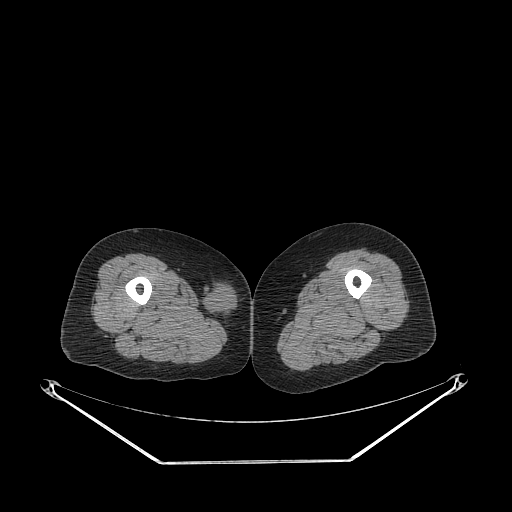
CT of an extremity soft-tissue mass (from a PET/CT study), one axial slice; slice 229 of 311 in the series (ordered by position); reconstruction kernel STANDARD; 140 kVp; soft-tissue window (W 400 / L 40 HU); 3.75 mm slice thickness; 512 × 512 image matrix. Female patient. Case-level facts recorded for this patient, not image findings: histological type: leiomyosarcoma; grade: intermediate; site of the primary tumour: parascapusular.
Outlined on this slice (expert contour drawn on MRI and transferred to this co-registered scan by the dataset authors):
- gross tumour volume including surrounding oedema: bounding box [x1, y1, x2, y2] px = [205, 278, 238, 318]
- gross tumour volume (mass): [205, 290, 238, 316]